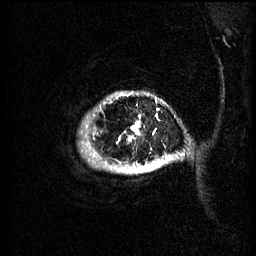
Breast MRI (dynamic contrast-enhanced), one sagittal slice. Slice 58 of 60 in the series (ordered by position). 3 images stored at this slice position (order not interpretable as contrast timing). 1.5 T. TE 4.2 ms, TR 11 ms. 256 × 256 image matrix, field of view 220 × 220 mm. Female patient, age 51 years.
Structures marked on this image (semi-automatic segmentation, software-assisted and operator-edited):
- analysis volume of interest (the breast-tissue region the enhancement analysis was run in; not a lesion): bounding box (x1, y1, x2, y2) in pixels: (92, 92, 172, 173)
- tumour enhancement mask (voxels above the 70 % enhancement threshold inside the analysis volume of interest): (132, 122, 167, 169)